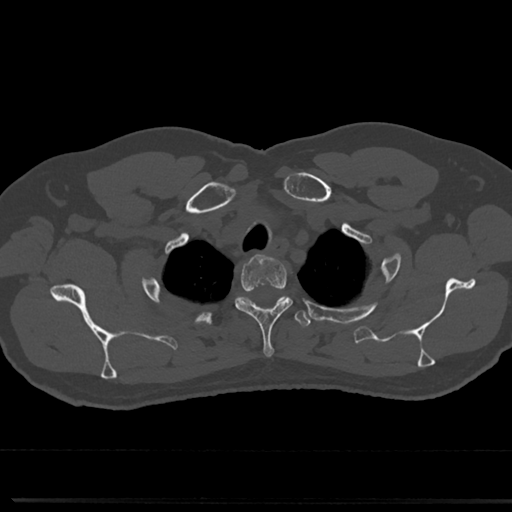
CT including the spine, one axial slice. Slice 625 of 817 in the series (ordered by position). Bone window (W 1800 / L 400 HU). 0.5 mm slice thickness. 512 × 512 image matrix, field of view 355 × 355 mm. Patient: male, 61 years. Case-level facts recorded for this patient, not image findings: primary cancer: prostate.
Structures marked on this image (semi-automatically segmented with operator editing):
- T1 vertebra: bounding box [x1, y1, x2, y2] px = [239, 297, 285, 304]
- T2 vertebra: [235, 256, 292, 357]
- T3 vertebra: [219, 297, 312, 329]